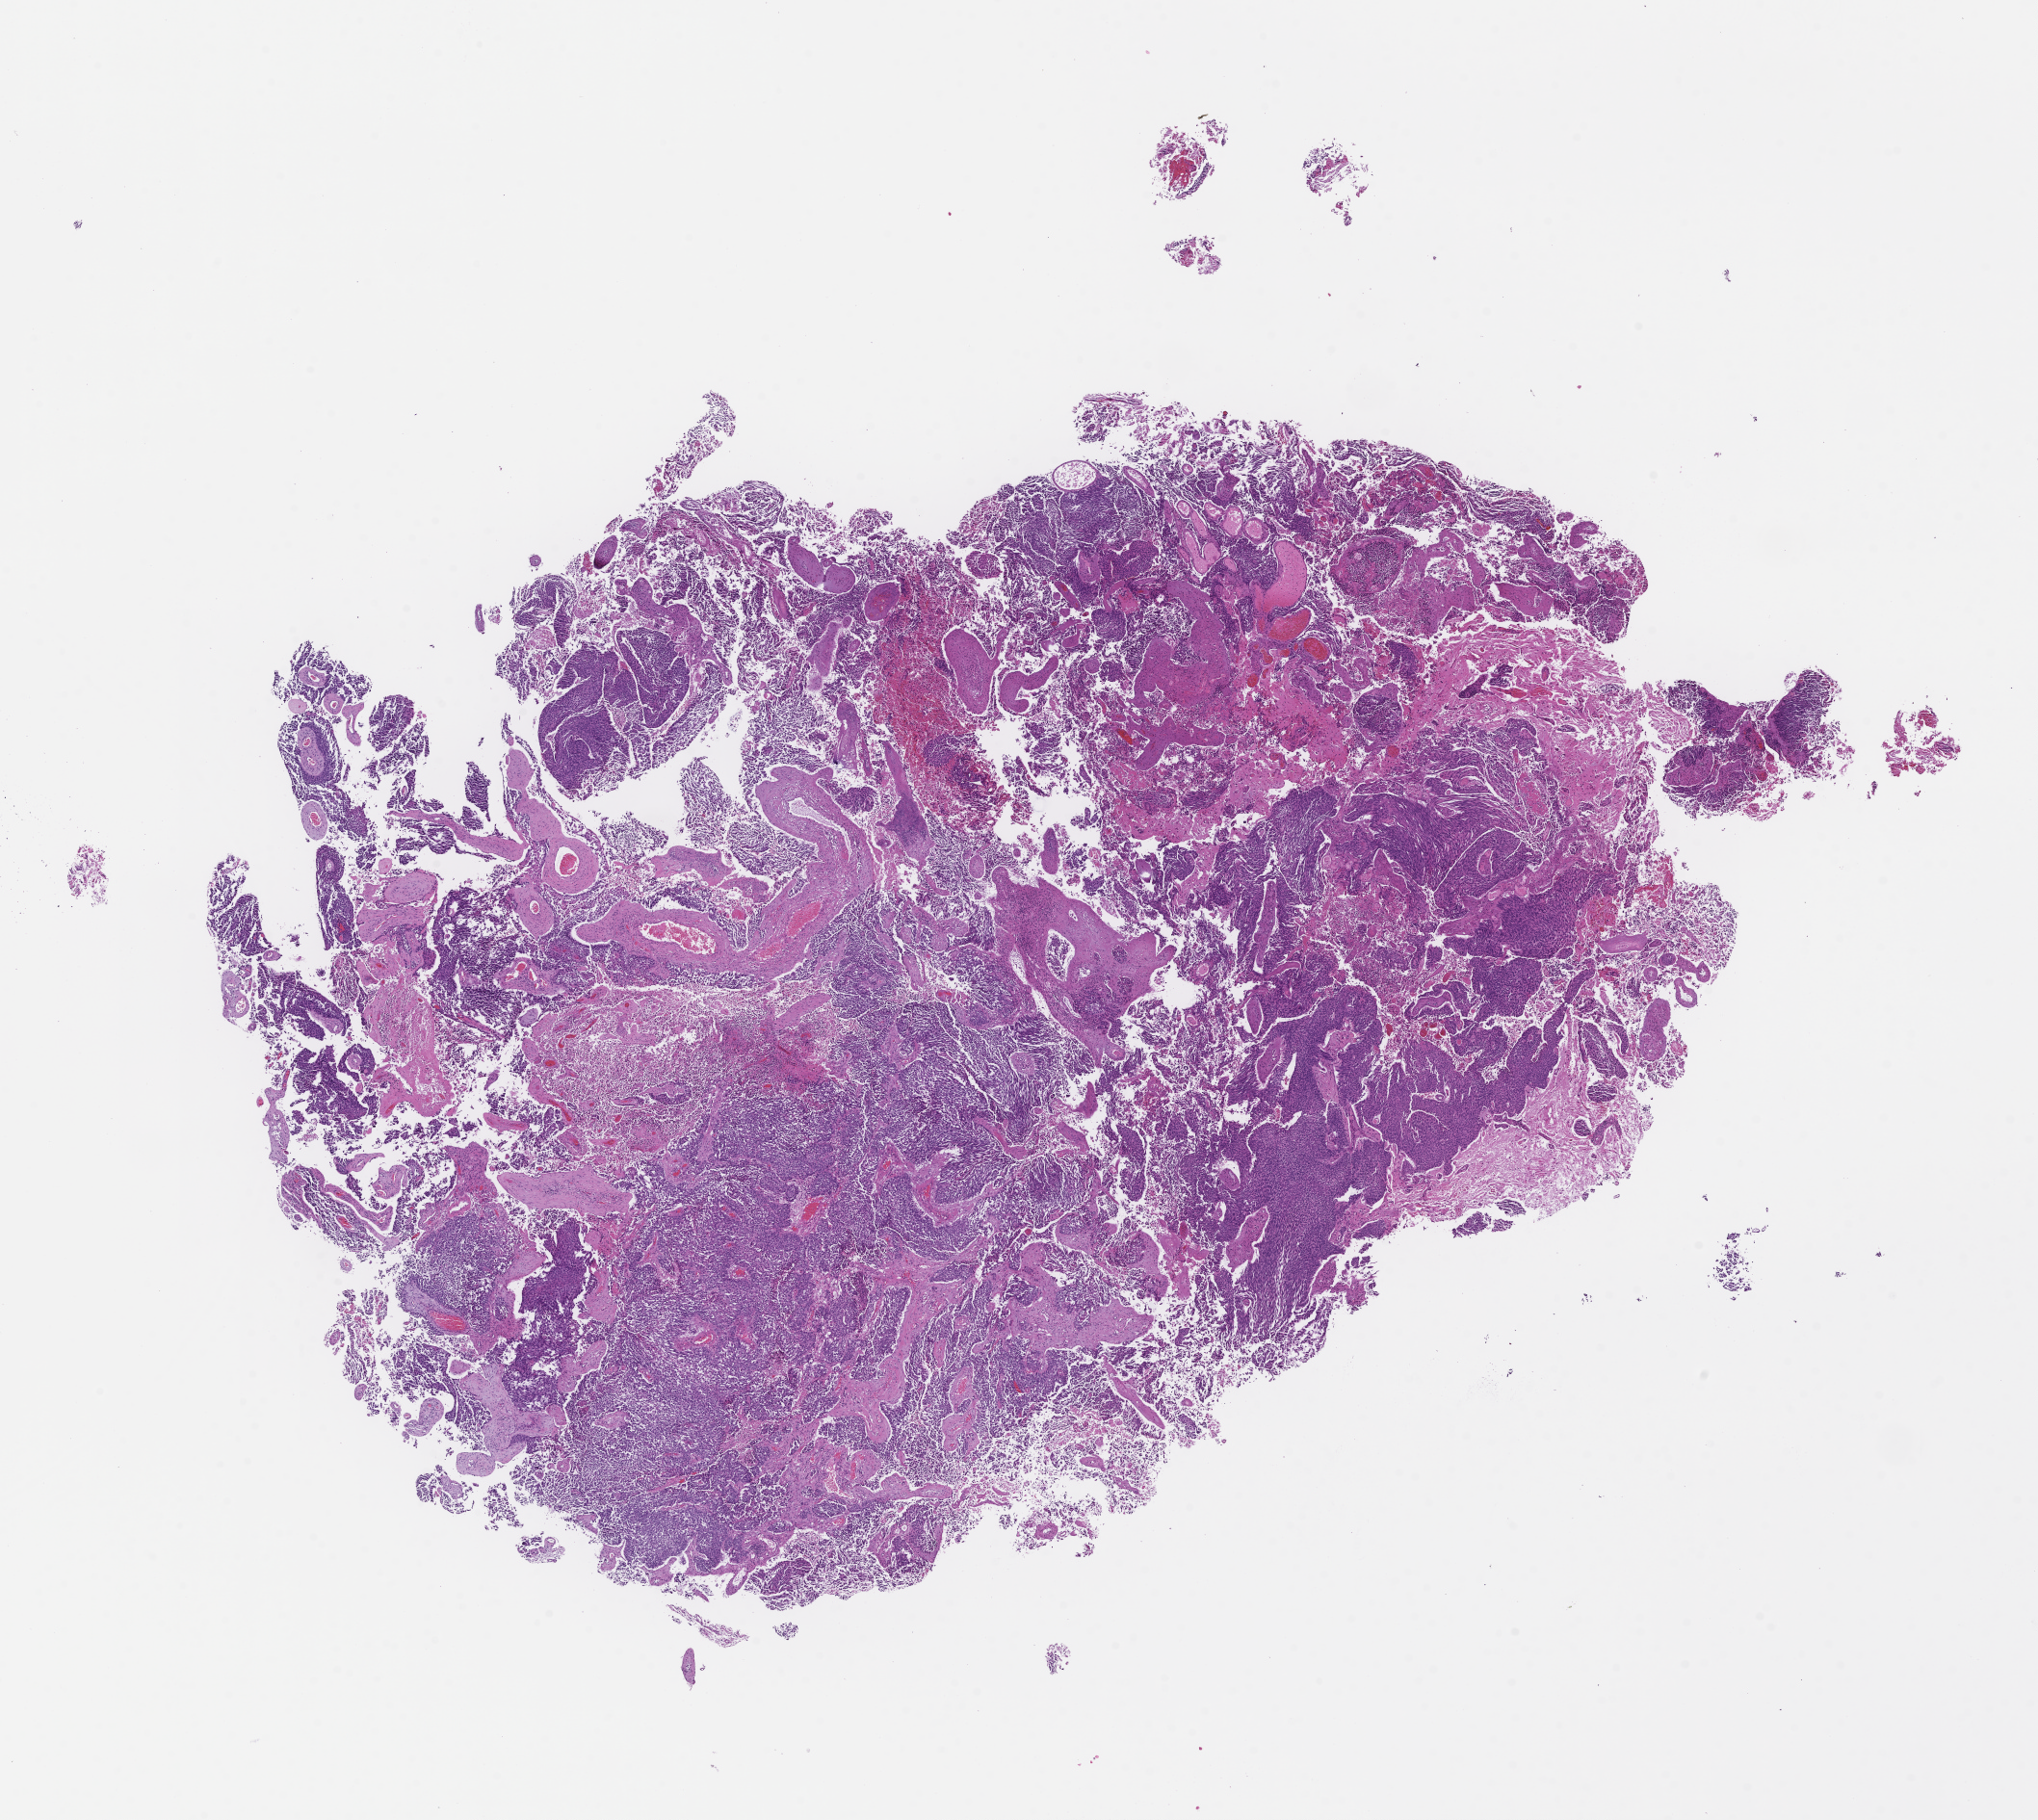
Whole-slide image, haematoxylin and eosin stain, a low-resolution overview of the entire scanned area, about 17.1 x 15.3 mm. Formalin-fixed paraffin-embedded section. Specimen time point: collected at baseline (before treatment). Patient: male.
This section: metastatic tumor tissue. Primary diagnosis of the patient: Non-Small Cell Lung Carcinoma.